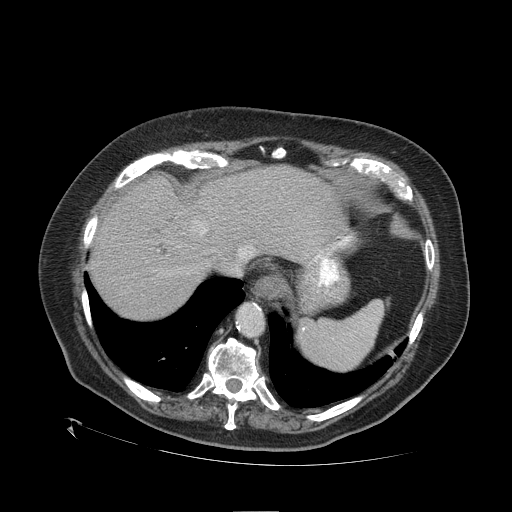
Contrast-enhanced abdominal CT (liver protocol), one axial slice; slice 89 of 109 in the series (ordered by position); reconstruction kernel STANDARD; 120 kVp; one of 2 acquisitions stored at this slice position; soft-tissue window (W 400 / L 40 HU); 2.5 mm slice thickness; 512 × 512 image matrix, field of view 460 × 460 mm. From the clinical record (not read from this slice): diagnosis: hepatocellular carcinoma (patient treated with transarterial chemoembolisation; whether this scan precedes or follows treatment is not stated here); TNM stage (as recorded): Stage-I; Child-Pugh class: A; tumour differentiation: no biopsy.
Annotated regions visible in this slice (semi-automatic segmentation, software-assisted and operator-edited):
- abdominal aorta: bounding box (x1, y1, x2, y2) in pixels: (238, 305, 264, 335)
- liver parenchyma outside the tumour (the mass and vessels are separate outlines, so this box may not span the whole liver): (92, 166, 356, 318)
- mass: (185, 215, 210, 240)
- liver vessels: (240, 236, 351, 259)